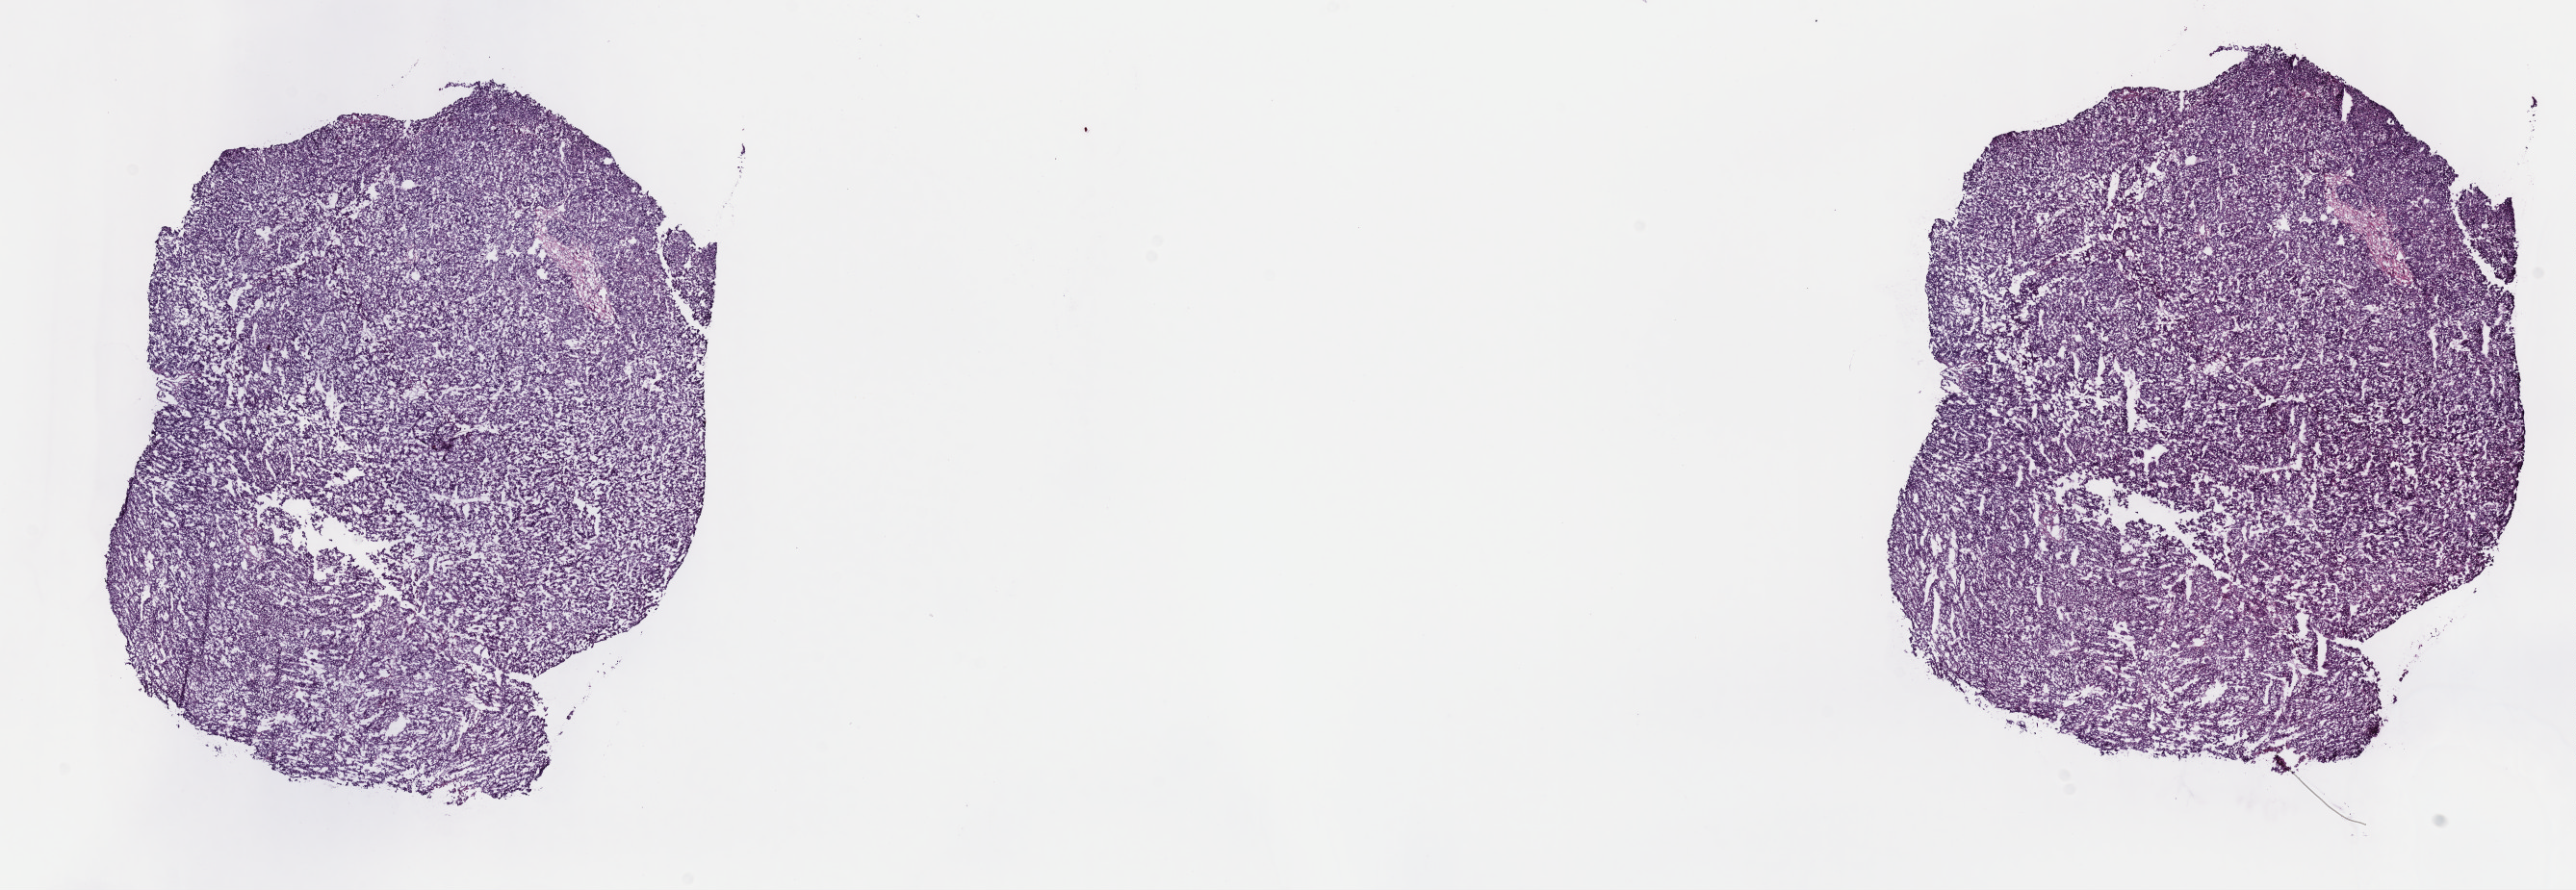
Digitized Hematoxylin and eosin (H&E) stained tissue section (whole slide), shown as a low-resolution overview of the whole scanned area (about 21.6 x 7.5 mm); frozen section from the top of the tissue portion; sample: primary tumour, liver. Patient: male, age at initial diagnosis 54 years. Composition of this section per pathologist review: tumour cells 94%, tumour nuclei 95%.
Histologic diagnosis: Hepatocellular carcinoma, NOS.